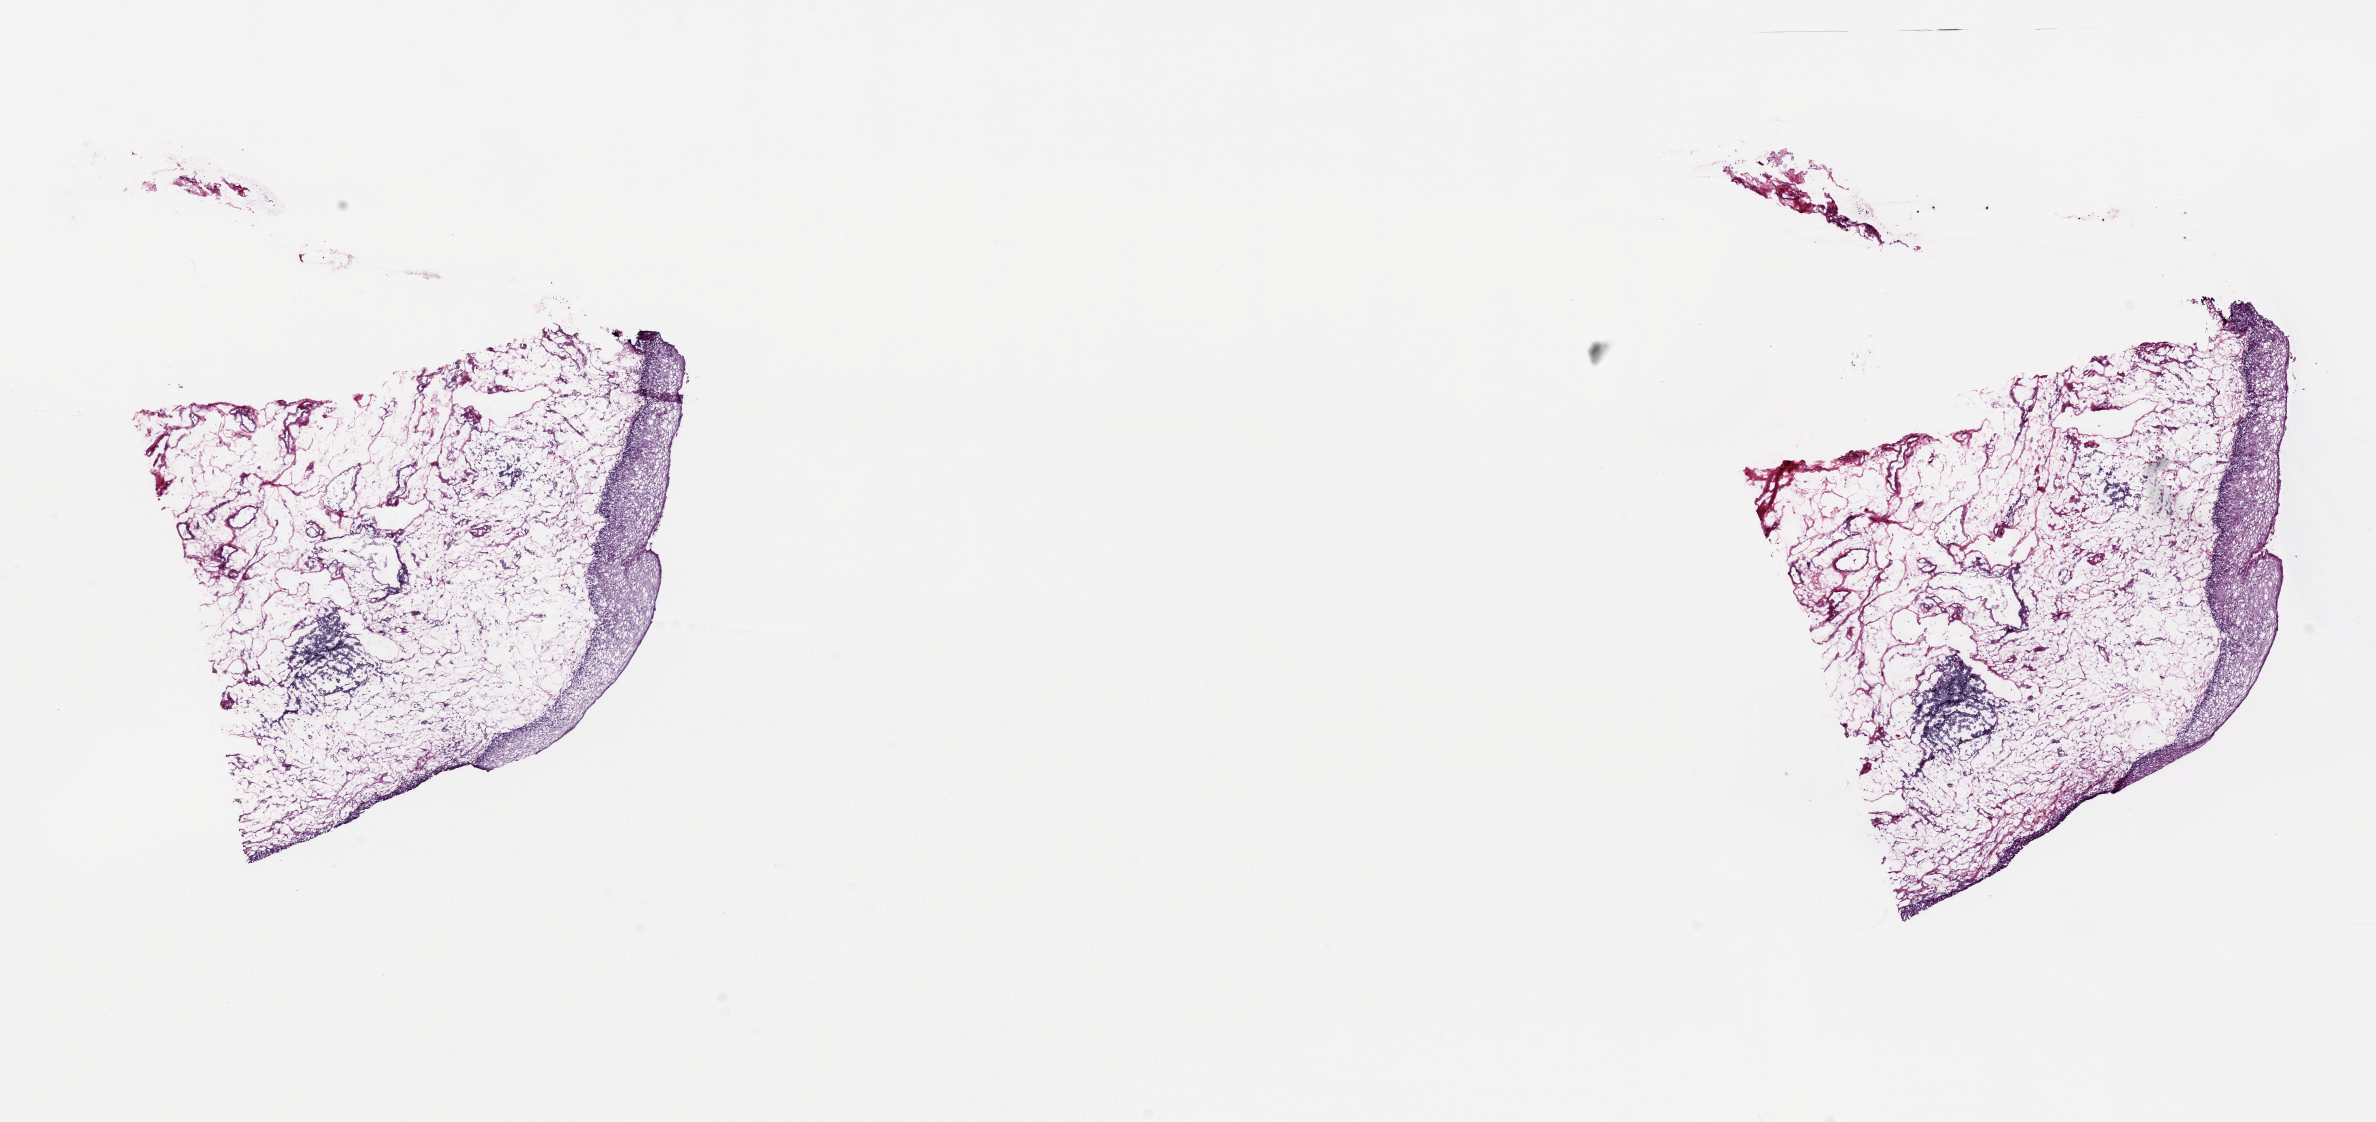
Digitized Hematoxylin and eosin (H&E) stained tissue section (whole slide), a low-resolution overview of the entire scanned area, about 18.8 x 8.9 mm (acquisition: 20x scan); frozen section from the top of the tissue portion; sample: solid tissue normal (non-tumour tissue), bladder. Patient: female, age at initial diagnosis 73 years. Pathologist review of this section (percent, as recorded): tumour cells 0%, tumour nuclei 0%, normal cells 20%, stromal cells 80%, necrosis 0%. Inflammatory infiltration, as recorded: lymphocyte infiltration 0%, monocyte infiltration 0%, neutrophil infiltration 0%.
• this section: solid tissue normal (non-tumour) sample from the same patient
• patient diagnosis: Transitional cell carcinoma (dome of bladder)